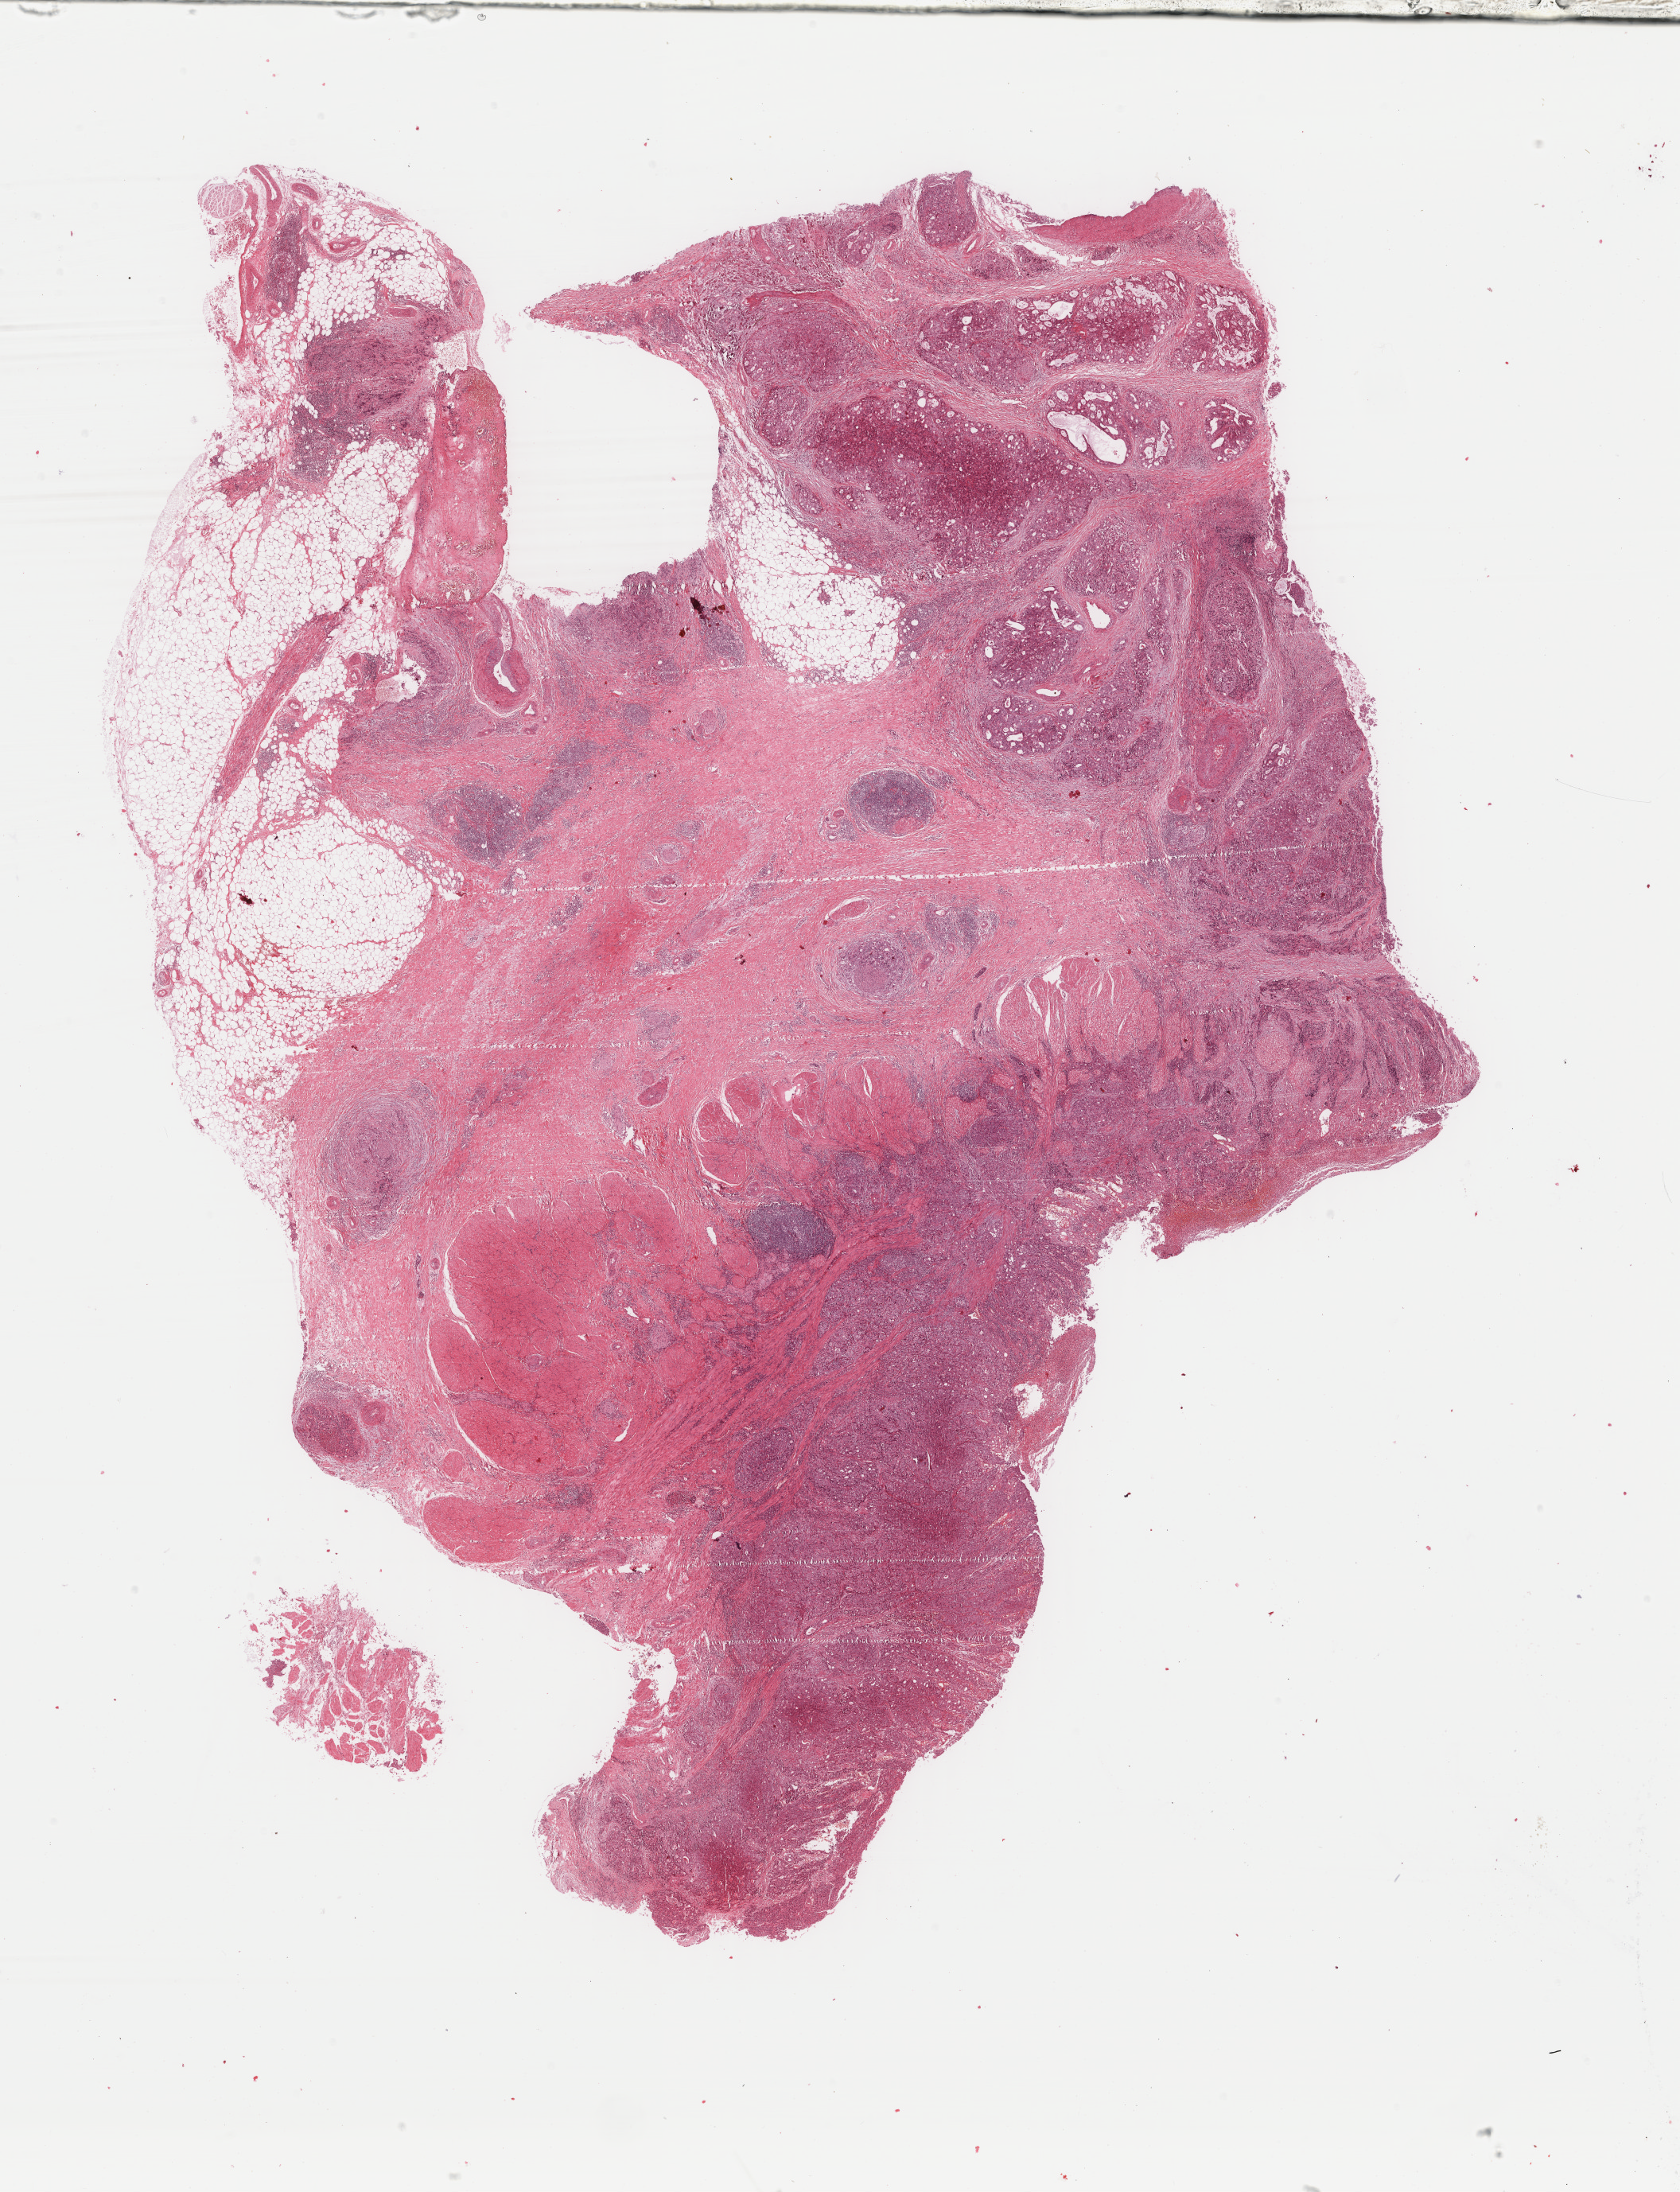
Whole-slide histology image, Hematoxylin and eosin (H&E) stained, shown as a low-resolution overview of the whole scanned area (about 16.8 x 21.9 mm), formalin-fixed paraffin-embedded (FFPE) diagnostic section, sample: primary tumour, stomach. Male patient; age at initial diagnosis 68 years. Histologic grade: G2 (moderately differentiated).
AJCC pathologic stage: IIA (7th edition). TNM: T3 N0 M0. Diagnosis: Adenocarcinoma, NOS (cardia, NOS).